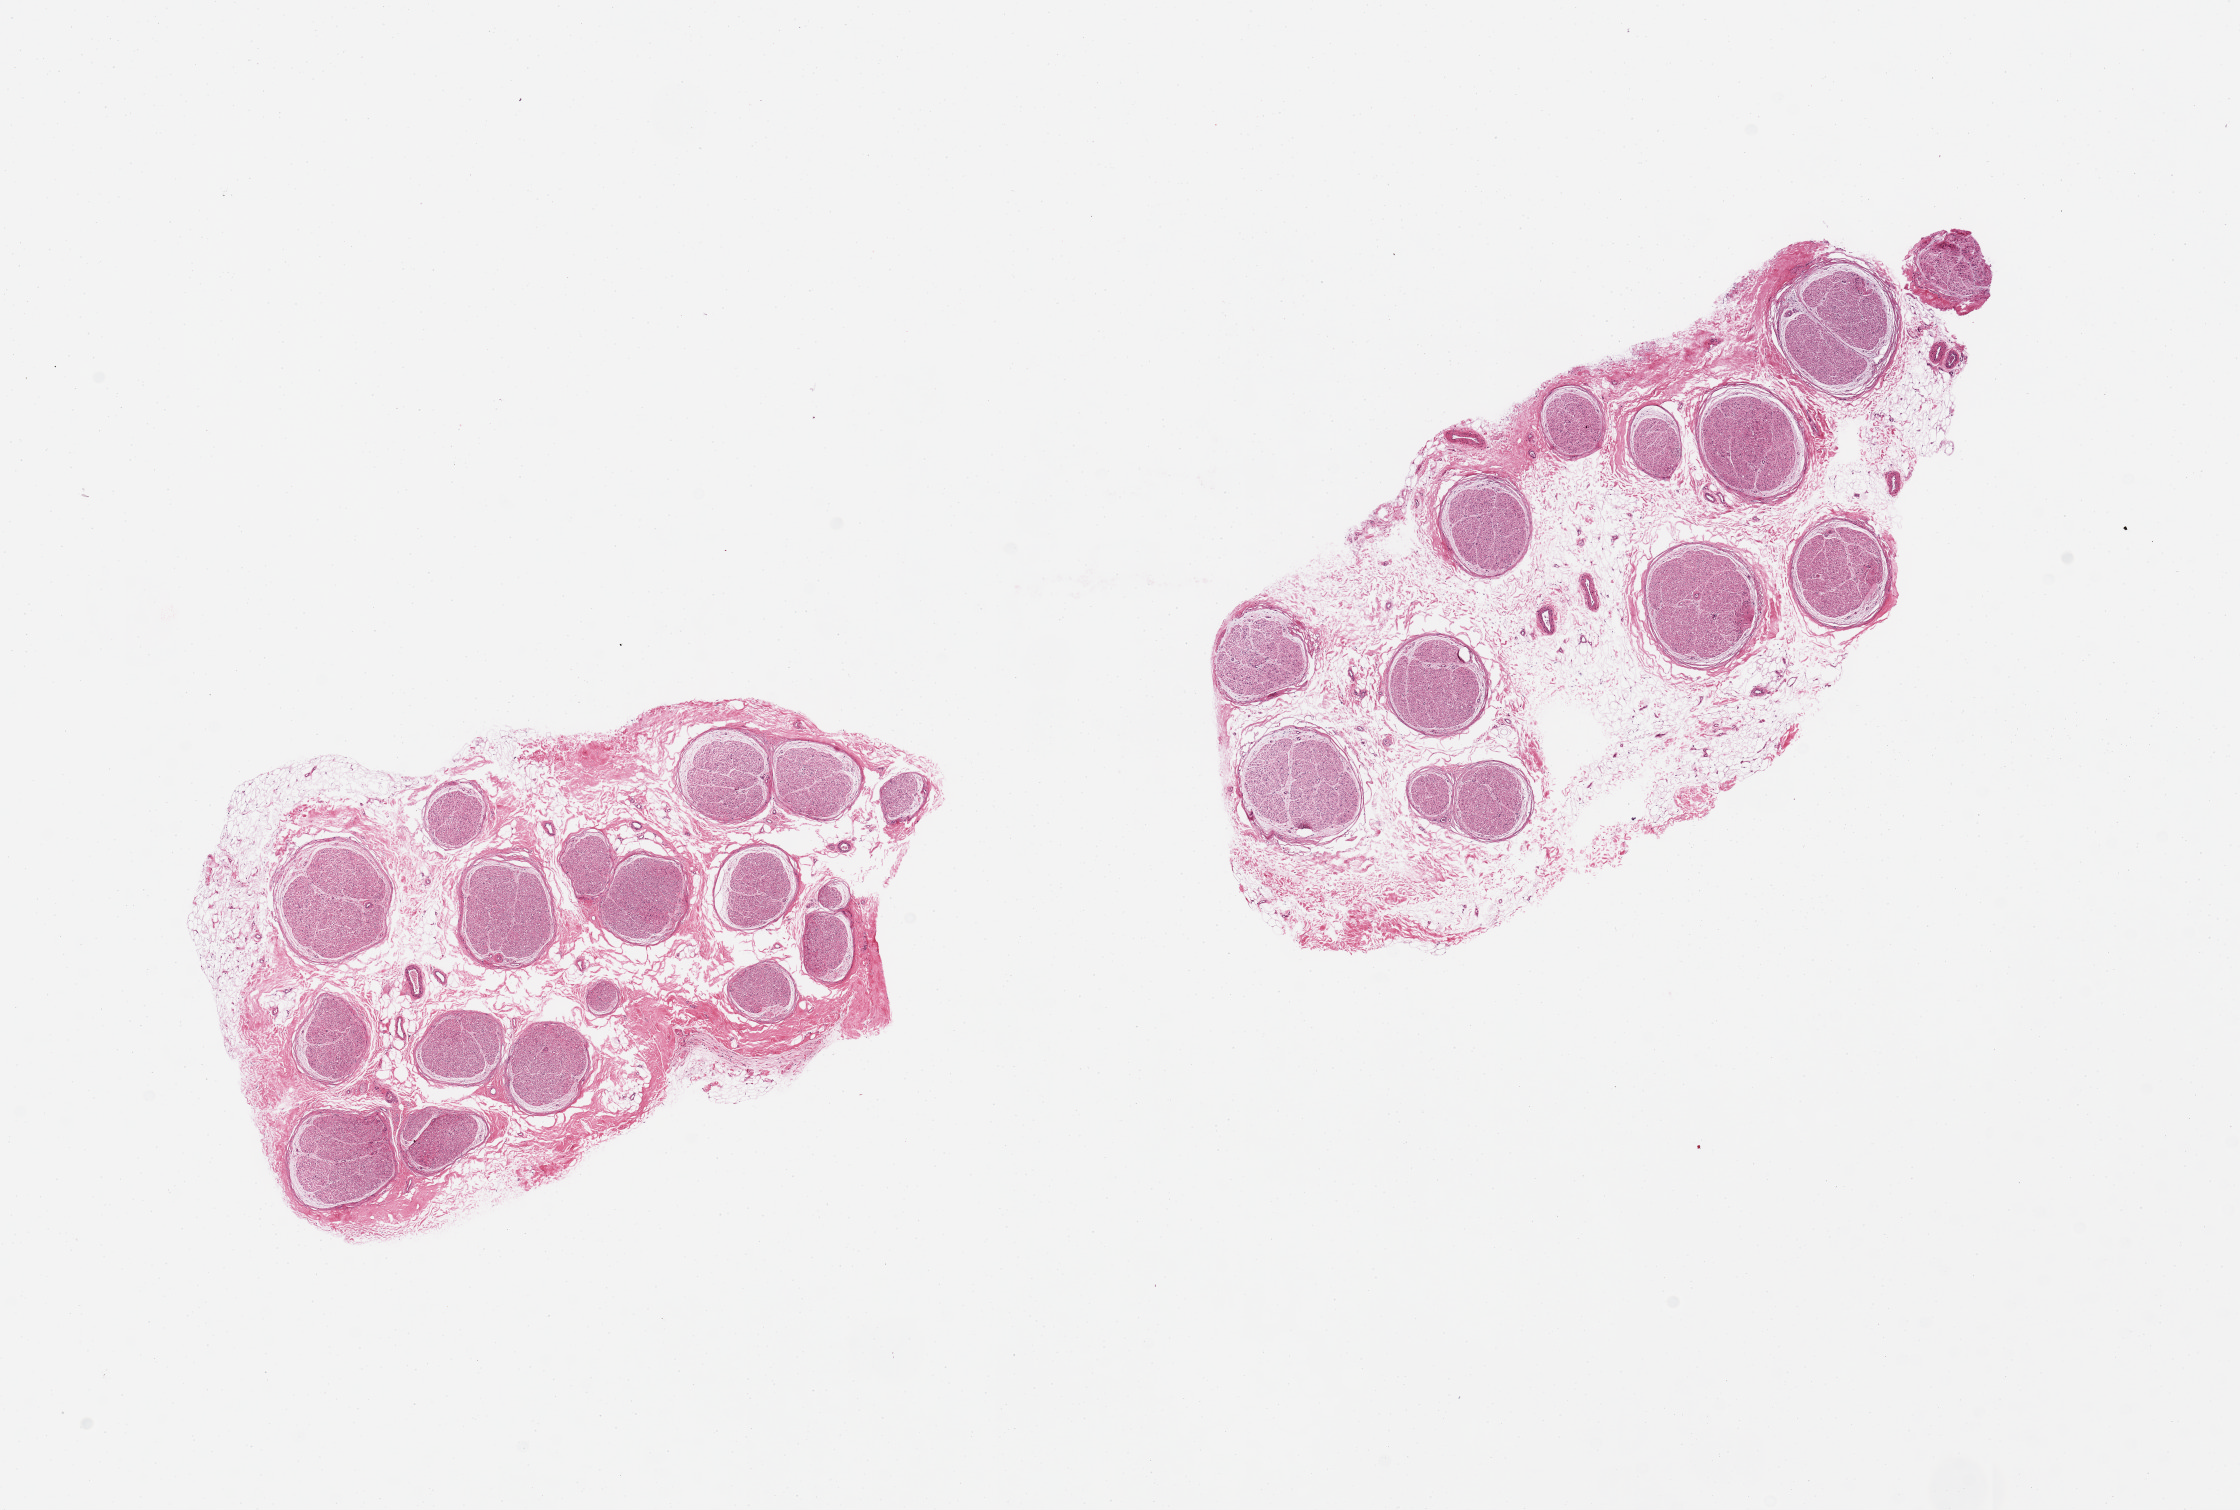
Digitized H&E-stained section, whole scanned area (about 17.7 x 11.9 mm, slide scanned at 20x) shown as a low-resolution overview, PAXgene-fixed, paraffin-embedded tissue, sampled site (target tissue): tibial nerve, tissue donor sample.
Reviewer comment on this tissue sample: 2 pieces; 50% internal edematous stroma and fat.